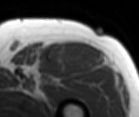
MRI of an extremity soft-tissue mass, one axial slice. MR volume resampled by the dataset authors to the PET/CT grid (not the native acquisition matrix). 139 × 117 image matrix, field of view 136 × 114 mm. Male patient. Case-level facts recorded for this patient, not image findings: histological type: extraskeletal osteosarcoma; grade: high; site of the primary tumour: thigh.
Structures marked on this image (expert contour drawn on MRI and transferred to this co-registered scan by the dataset authors):
- gross tumour volume (mass): bounding box [x1, y1, x2, y2] px = [49, 41, 103, 69]